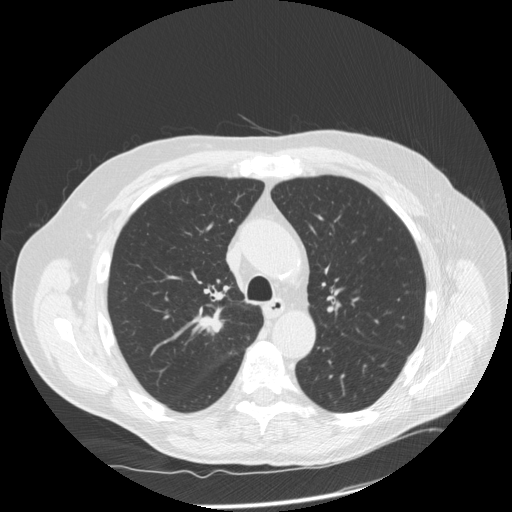
Low-dose screening chest CT, one axial slice. Slice 114 of 166 in the series (ordered by position). Reconstruction kernel STANDARD. 120 kVp. Lung window (W 1500 / L -600 HU). 2.5 mm slice thickness. 512 × 512 image matrix, field of view 390 × 390 mm.
Annotated regions visible in this slice (outlined manually by an expert reader):
- lesion 1 (tumor, upper lobe of right lung): bounding box (x1, y1, x2, y2) in pixels: (199, 314, 222, 332)